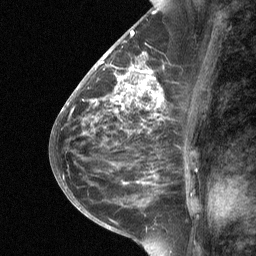
Breast MRI (dynamic contrast-enhanced), one sagittal slice; dynamic contrast-enhanced study with each time point stored as its own series, time point 2 of 3 at this slice position (early post-contrast, ordered by acquisition time); 1.5 T; TE 4.8 ms, TR 27 ms; 2 mm slice thickness; 256 × 256 image matrix, field of view 180 × 180 mm. Patient: female, 59 years. From the clinical record (not read from this slice): setting: breast cancer imaged before/during neoadjuvant chemotherapy; receptor status: triple-negative.
Structures marked on this image (semi-automatic segmentation, software-assisted and operator-edited):
- analysis volume of interest (the breast-tissue region the enhancement analysis was run in; not a lesion): bounding box <113,66,161,119> (left, top, right, bottom; pixels)
- tumour enhancement mask (voxels above the 90 % enhancement threshold inside the analysis volume of interest): <117,66,160,109>